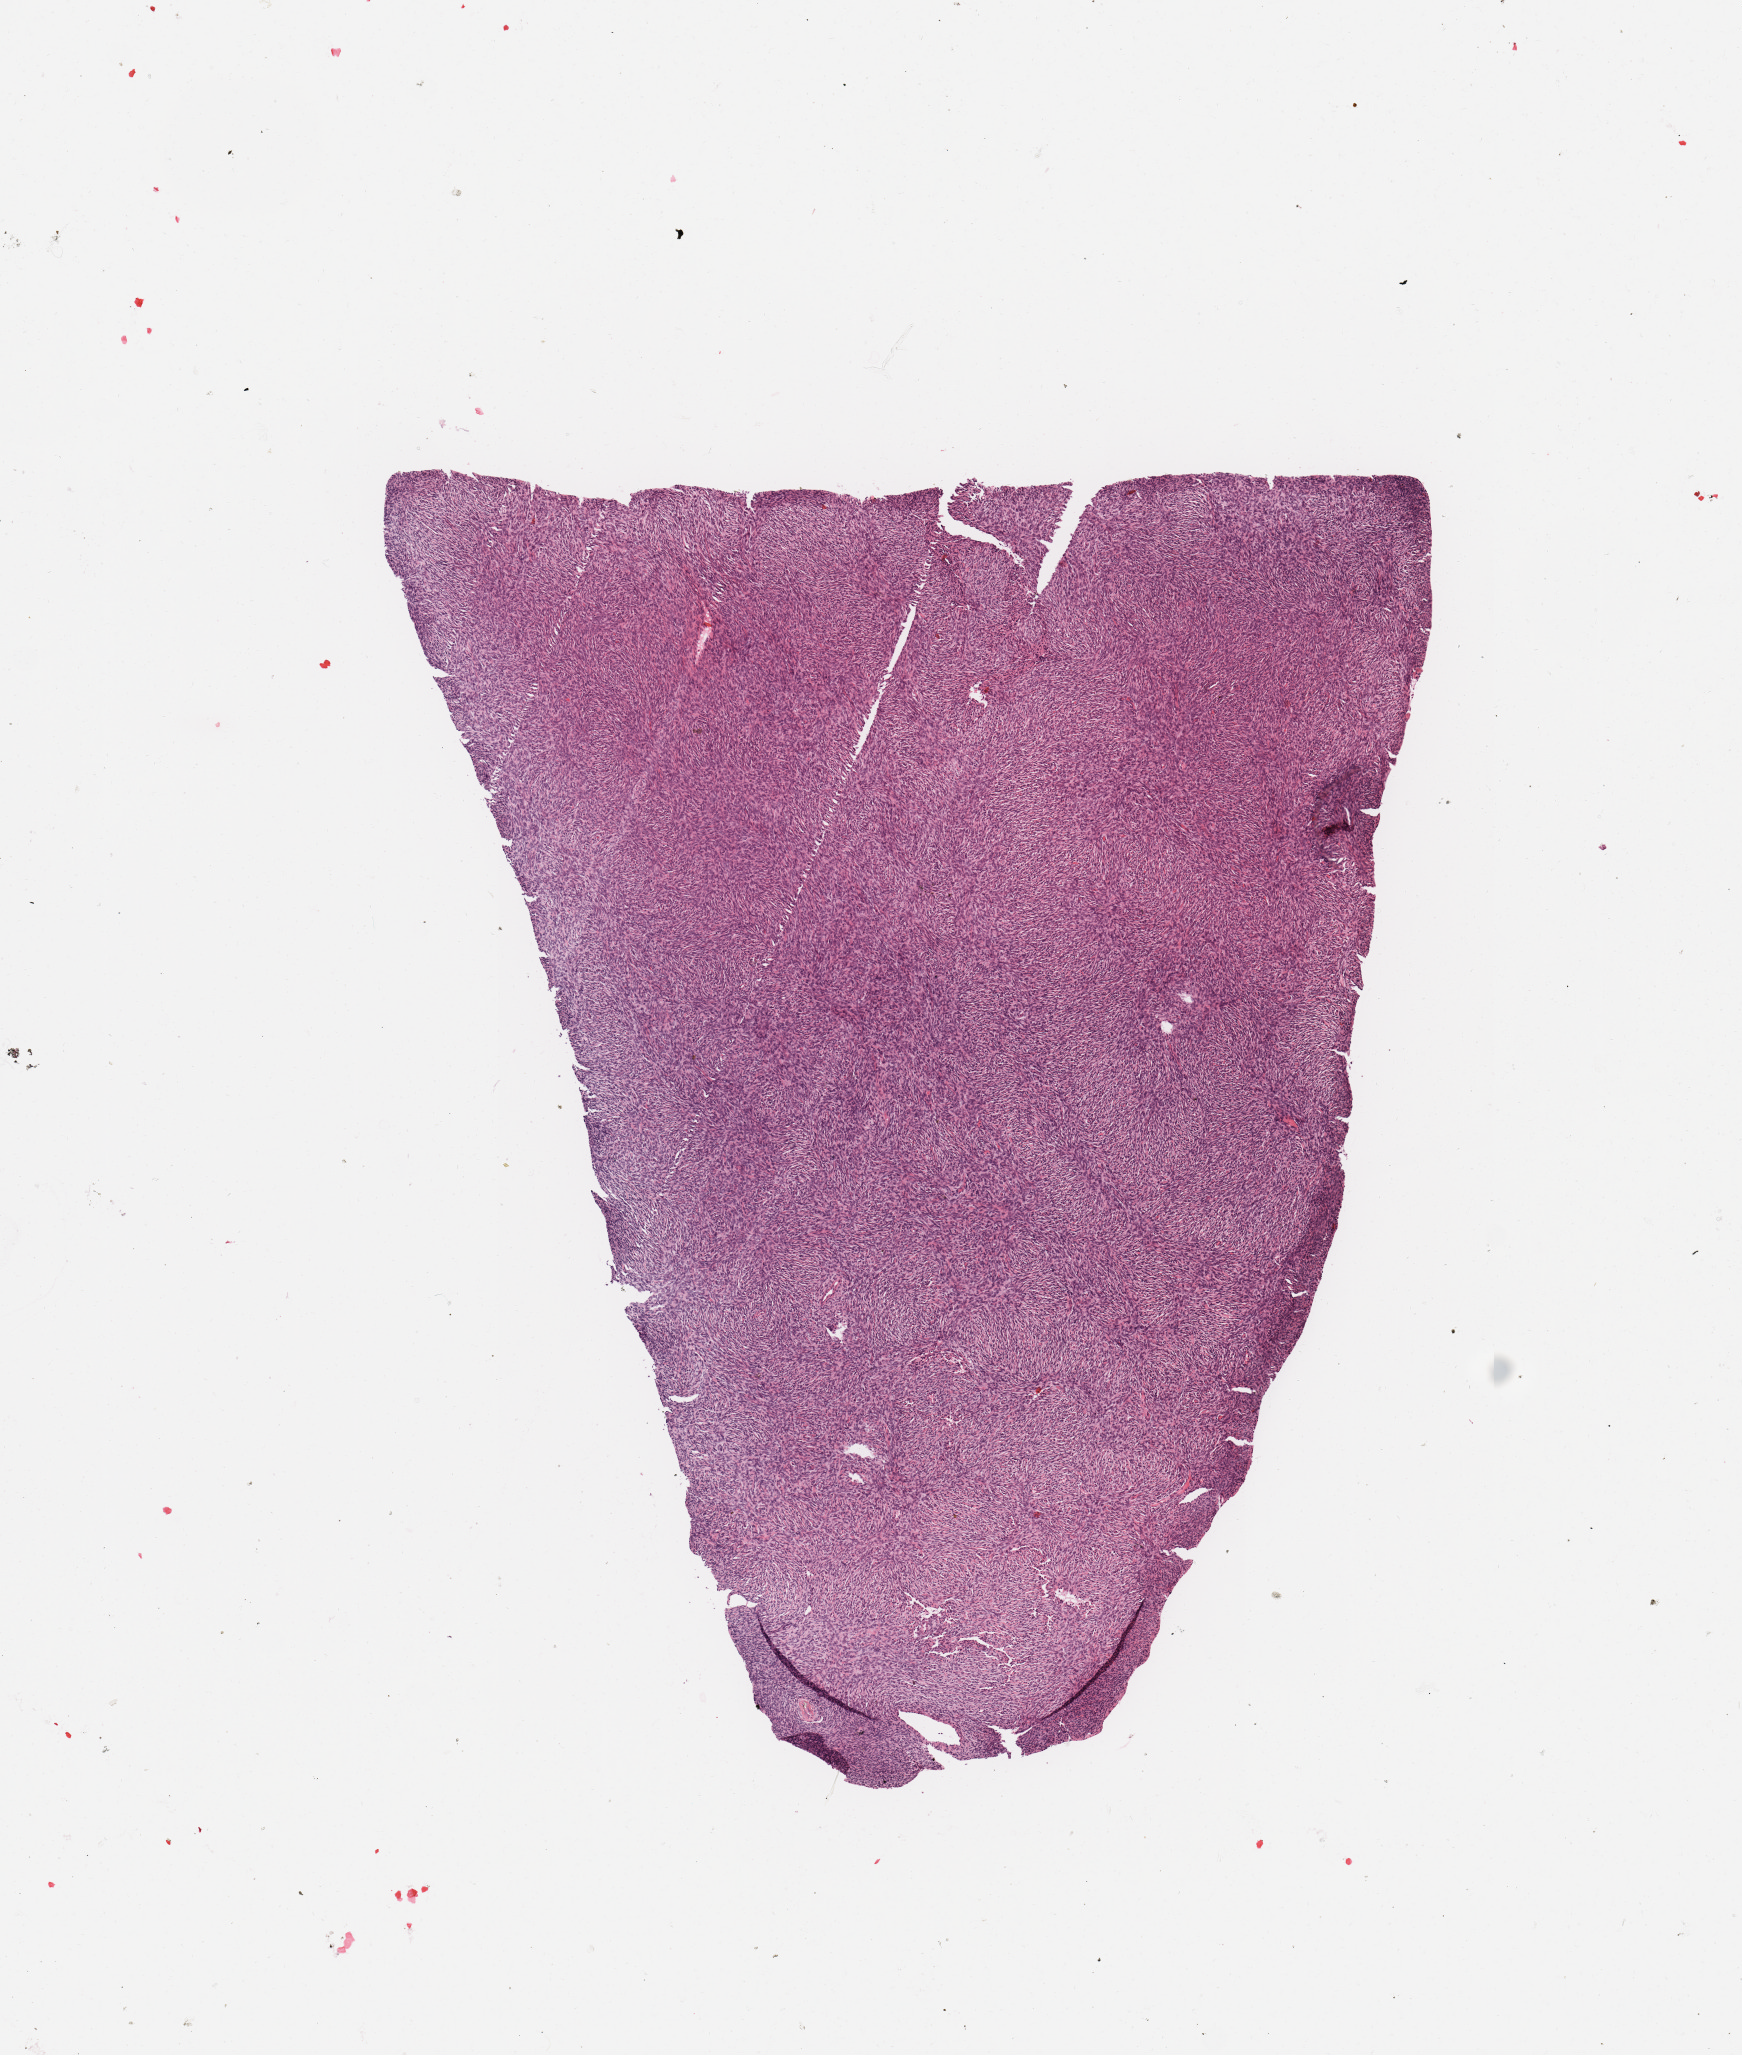
Hematoxylin and eosin (H&E) stained whole-slide image, whole scanned area (about 6.9 x 8.1 mm, slide scanned at 20x) shown as a low-resolution overview, tumour tissue sample. 42-year-old male patient.
Patient diagnosis (cohort enrolment): sarcoma (site not recorded at cohort level).